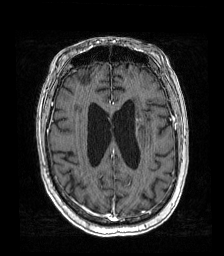
Brain MRI from a brain-tumour surgery series, one axial slice; position 63 of 192 along the scan axis; T1-weighted post-contrast; 224 × 256 image matrix, field of view 219 × 250 mm. From the clinical record (not read from this slice): histopathology: Metastatic carcinoma from lung primary; tumour location: Left Frontal Caudate.
Structures marked on this image (expert manual segmentation):
- tumour: bounding box [x1, y1, x2, y2] px = [117, 118, 148, 135]